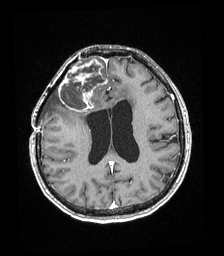
Brain MRI from a brain-tumour surgery series, one axial slice; slice 81 of 192 in the series (ordered by position); T1-weighted post-contrast; 1 mm slice thickness; 224 × 256 image matrix. From the clinical record (not read from this slice): histopathology: Astrocytoma; WHO grade: 4; IDH mutation: yes.
Annotated regions visible in this slice (outlined manually by an expert reader):
- tumour: box from (x=59, y=60) to (x=107, y=112) px